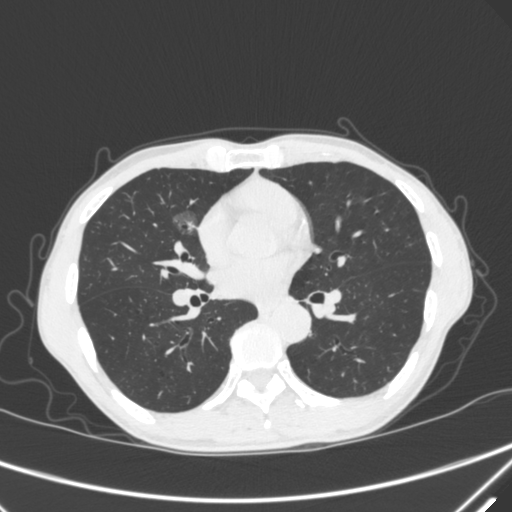
Chest CT, one axial slice; 120 kVp; lung window (W 1500 / L -600 HU); 1 mm slice thickness; 512 × 512 image matrix, field of view 350 × 350 mm. Patient: male, 67 years. From the clinical record (not read from this slice): clinical TNM (as recorded): T1c N0 M0; histopathological grade: G1-2.
Outlined on this slice (rectangle marked by the reading radiologist):
- lung tumour (recorded histology: adenocarcinoma): bounding box [x1, y1, x2, y2] px = [169, 207, 202, 245]